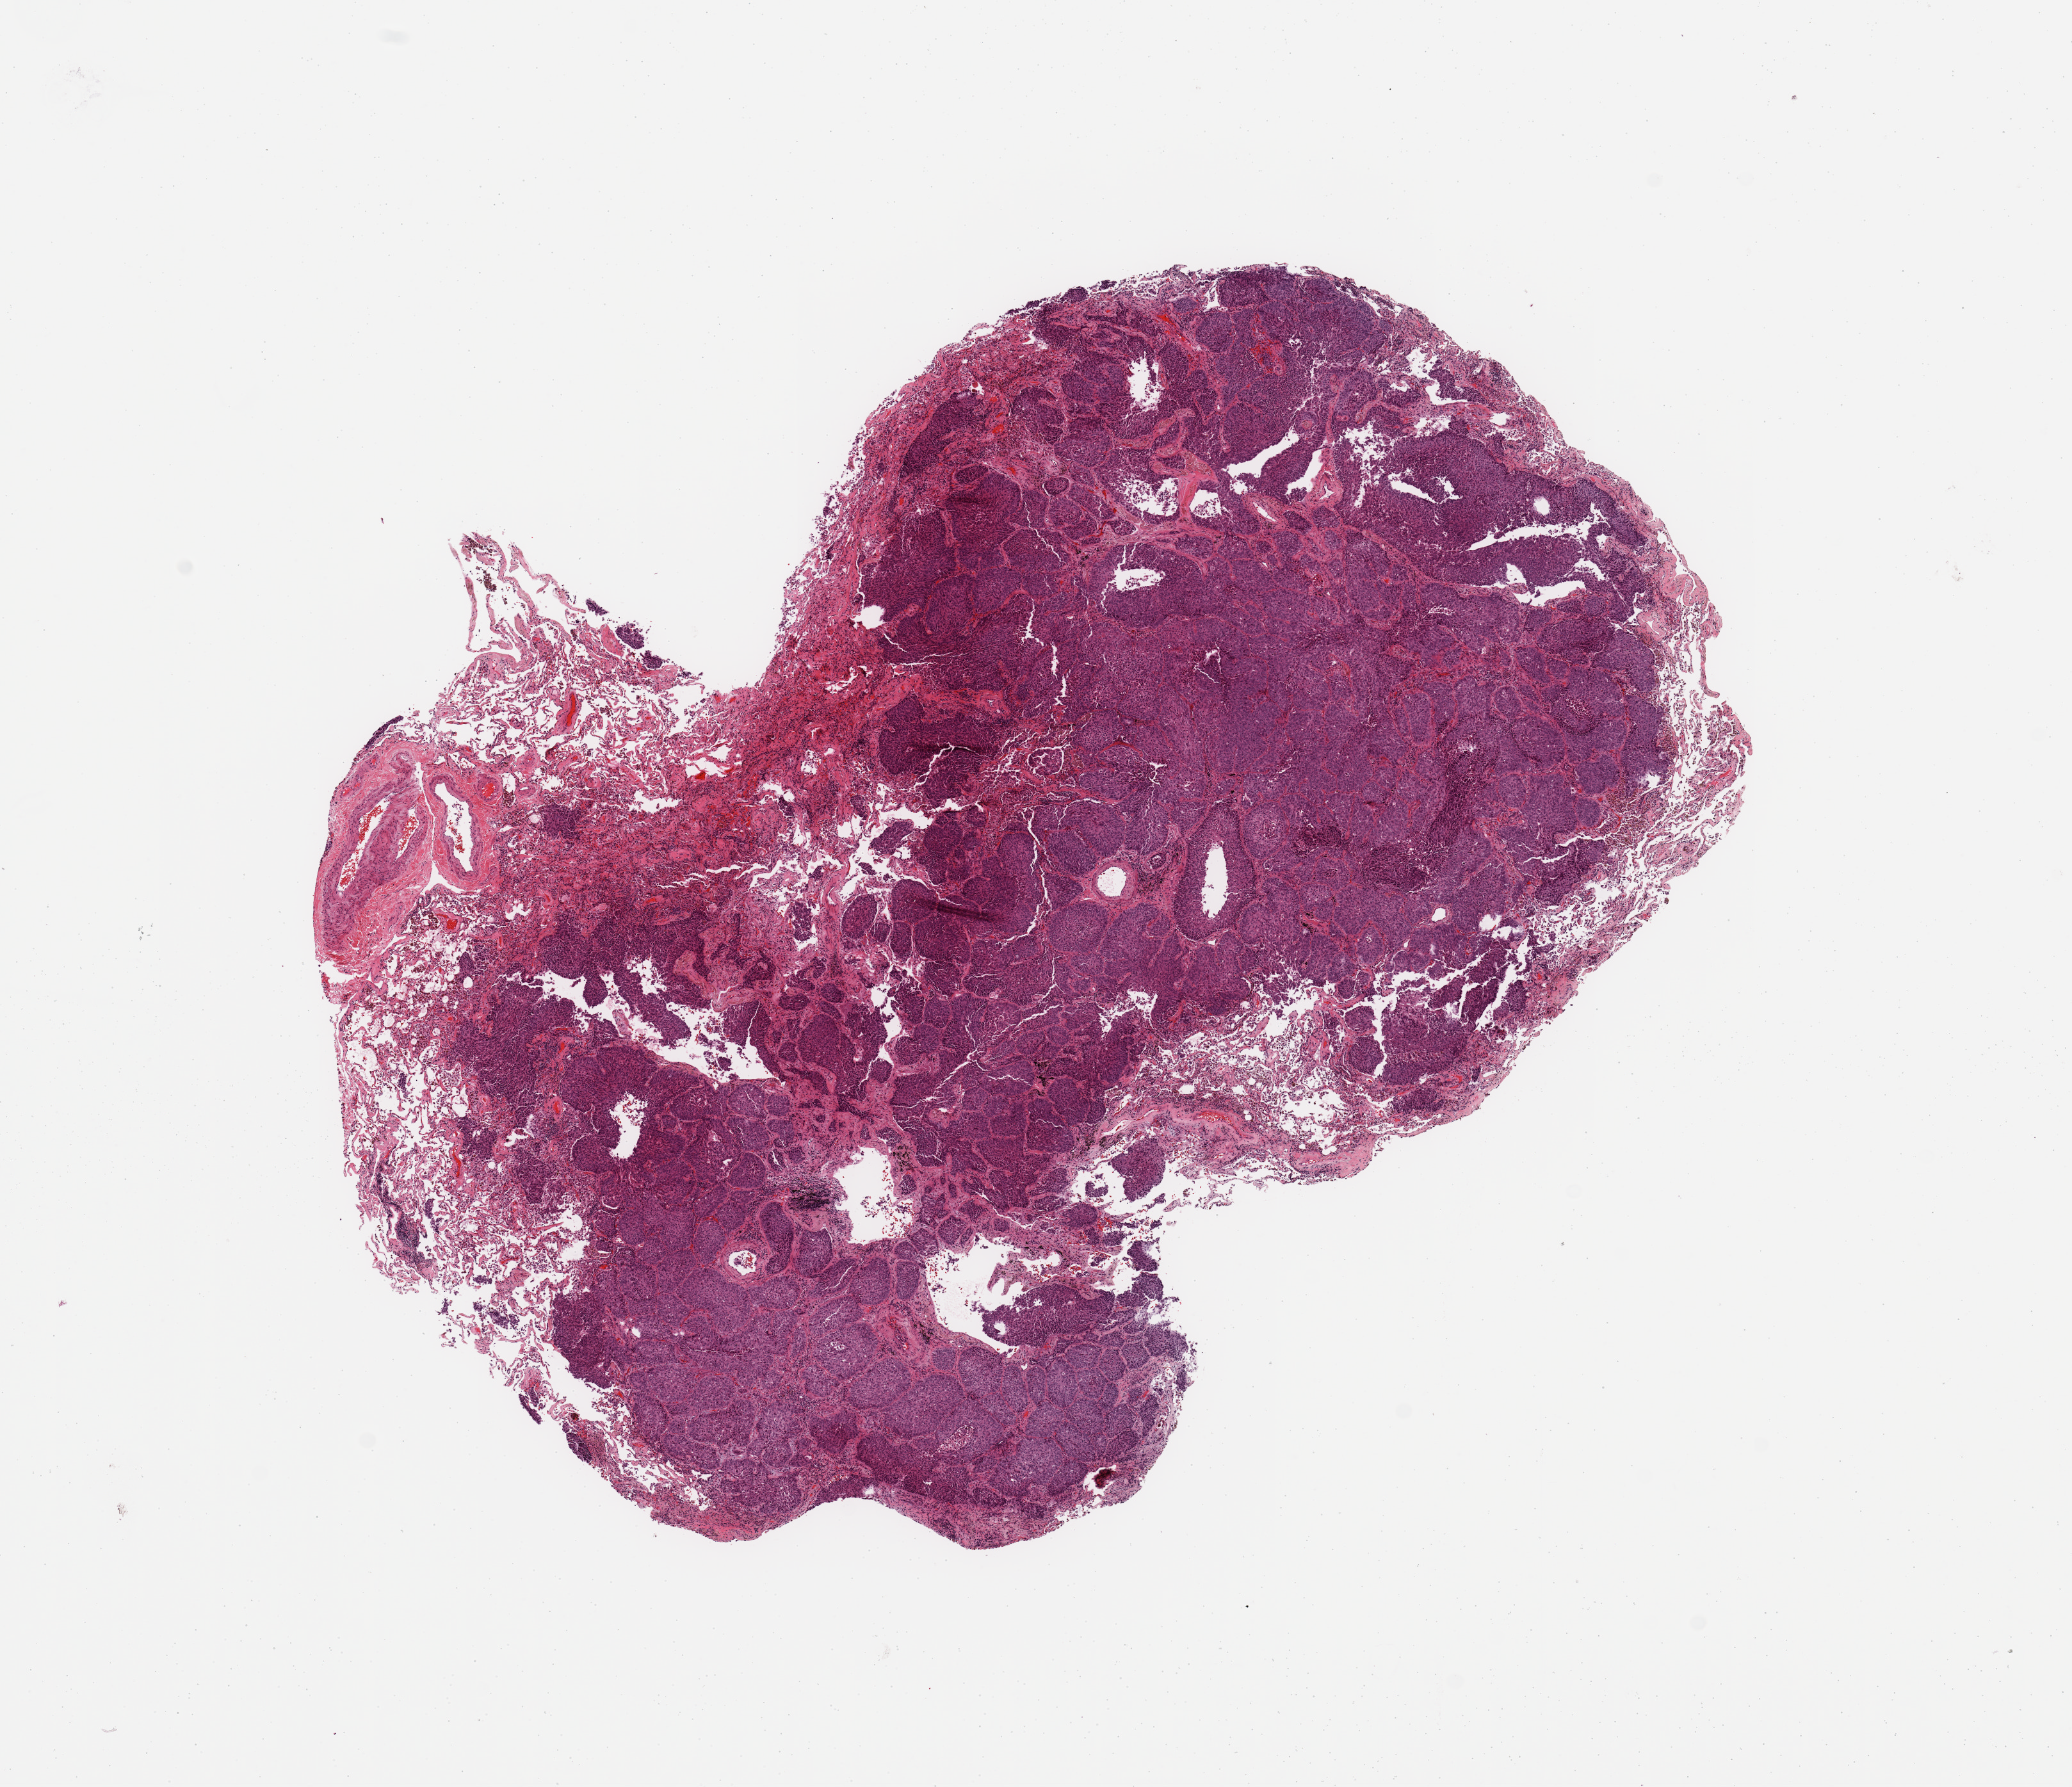
Digitized H&E tissue section (whole slide), low-resolution overview of the scanned area, about 12.8 x 11.0 mm (slide scanned at 20x), tumour tissue sample, sampled site: lung. 81-year-old female patient. Histologic grade: G2 (moderately differentiated). Pathologist review of this section (percent, as recorded): tumour nuclei 85%, necrosis 2%.
Primary tumour site (as recorded): right upper lobe. Histologic diagnosis: Squamous cell carcinoma, NOS. AJCC pathologic stage: IA.